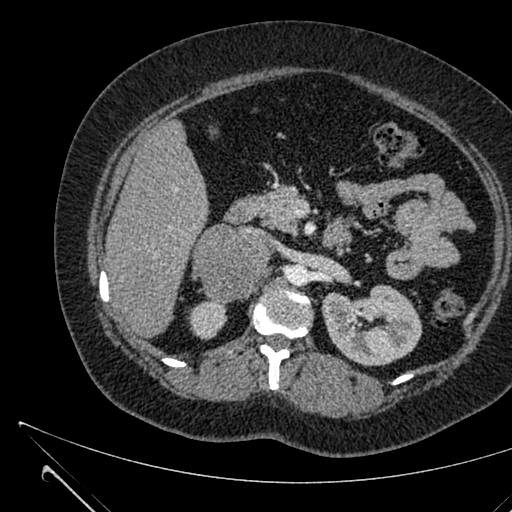
Contrast-enhanced abdominal CT, one axial slice; slice 382 of 731 in the series (ordered by position); intravenous contrast given; soft-tissue window (W 400 / L 40 HU); 512 × 512 image matrix, field of view 376 × 376 mm. Female patient, age 36 years. Case-level facts recorded for this patient, not image findings: diagnosis: adrenocortical carcinoma; tumour side: right adrenal; tumour size at pathology: 10 cm.
Annotated regions visible in this slice (semi-automatically segmented with operator editing):
- mass: bounding box <196,224,268,304> (left, top, right, bottom; pixels)